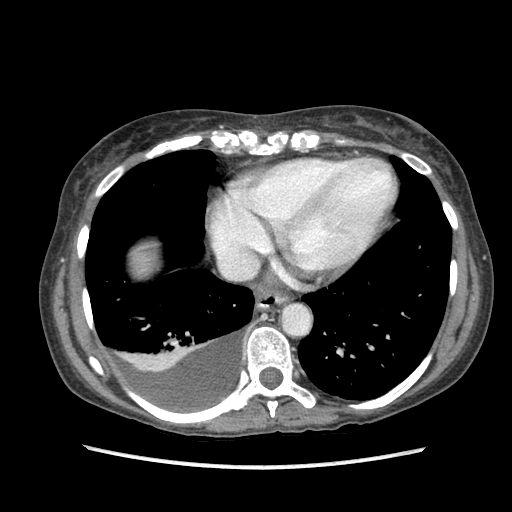
Contrast-enhanced abdominal CT (liver protocol), one axial slice; slice 83 of 87 in the series (ordered by position); 120 kVp; soft-tissue window (W 400 / L 40 HU); 2.5 mm slice thickness; 512 × 512 image matrix. Case-level facts recorded for this patient, not image findings: diagnosis: hepatocellular carcinoma (patient treated with transarterial chemoembolisation; whether this scan precedes or follows treatment is not stated here); TNM stage (as recorded): Stage-IIIB; Child-Pugh class: A; tumour differentiation: no biopsy; tumour nodularity: uninodular.
Structures marked on this image (semi-automatically segmented with operator editing):
- liver parenchyma outside the tumour (the mass and vessels are separate outlines, so this box may not span the whole liver): bounding box (x1, y1, x2, y2) in pixels: (132, 246, 154, 272)